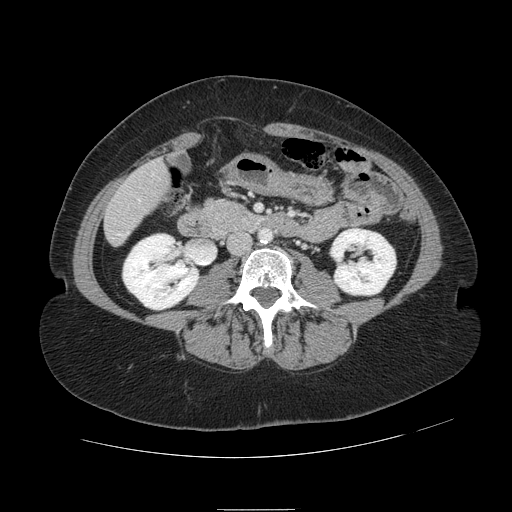
Contrast-enhanced abdominal CT, one axial slice. Position 15 of 121 along the scan axis. 120 kVp. Soft-tissue window (W 400 / L 40 HU). 512 × 512 image matrix, field of view 400 × 400 mm. Female patient, age 52 years. Case-level facts recorded for this patient, not image findings: diagnosis: colorectal cancer liver metastases, imaged before liver resection; multiple liver metastases: yes.
Annotated regions visible in this slice (manually delineated by an expert):
- hepatic veins: bounding box <119,174,154,236> (left, top, right, bottom; pixels)
- liver: <106,162,168,243>